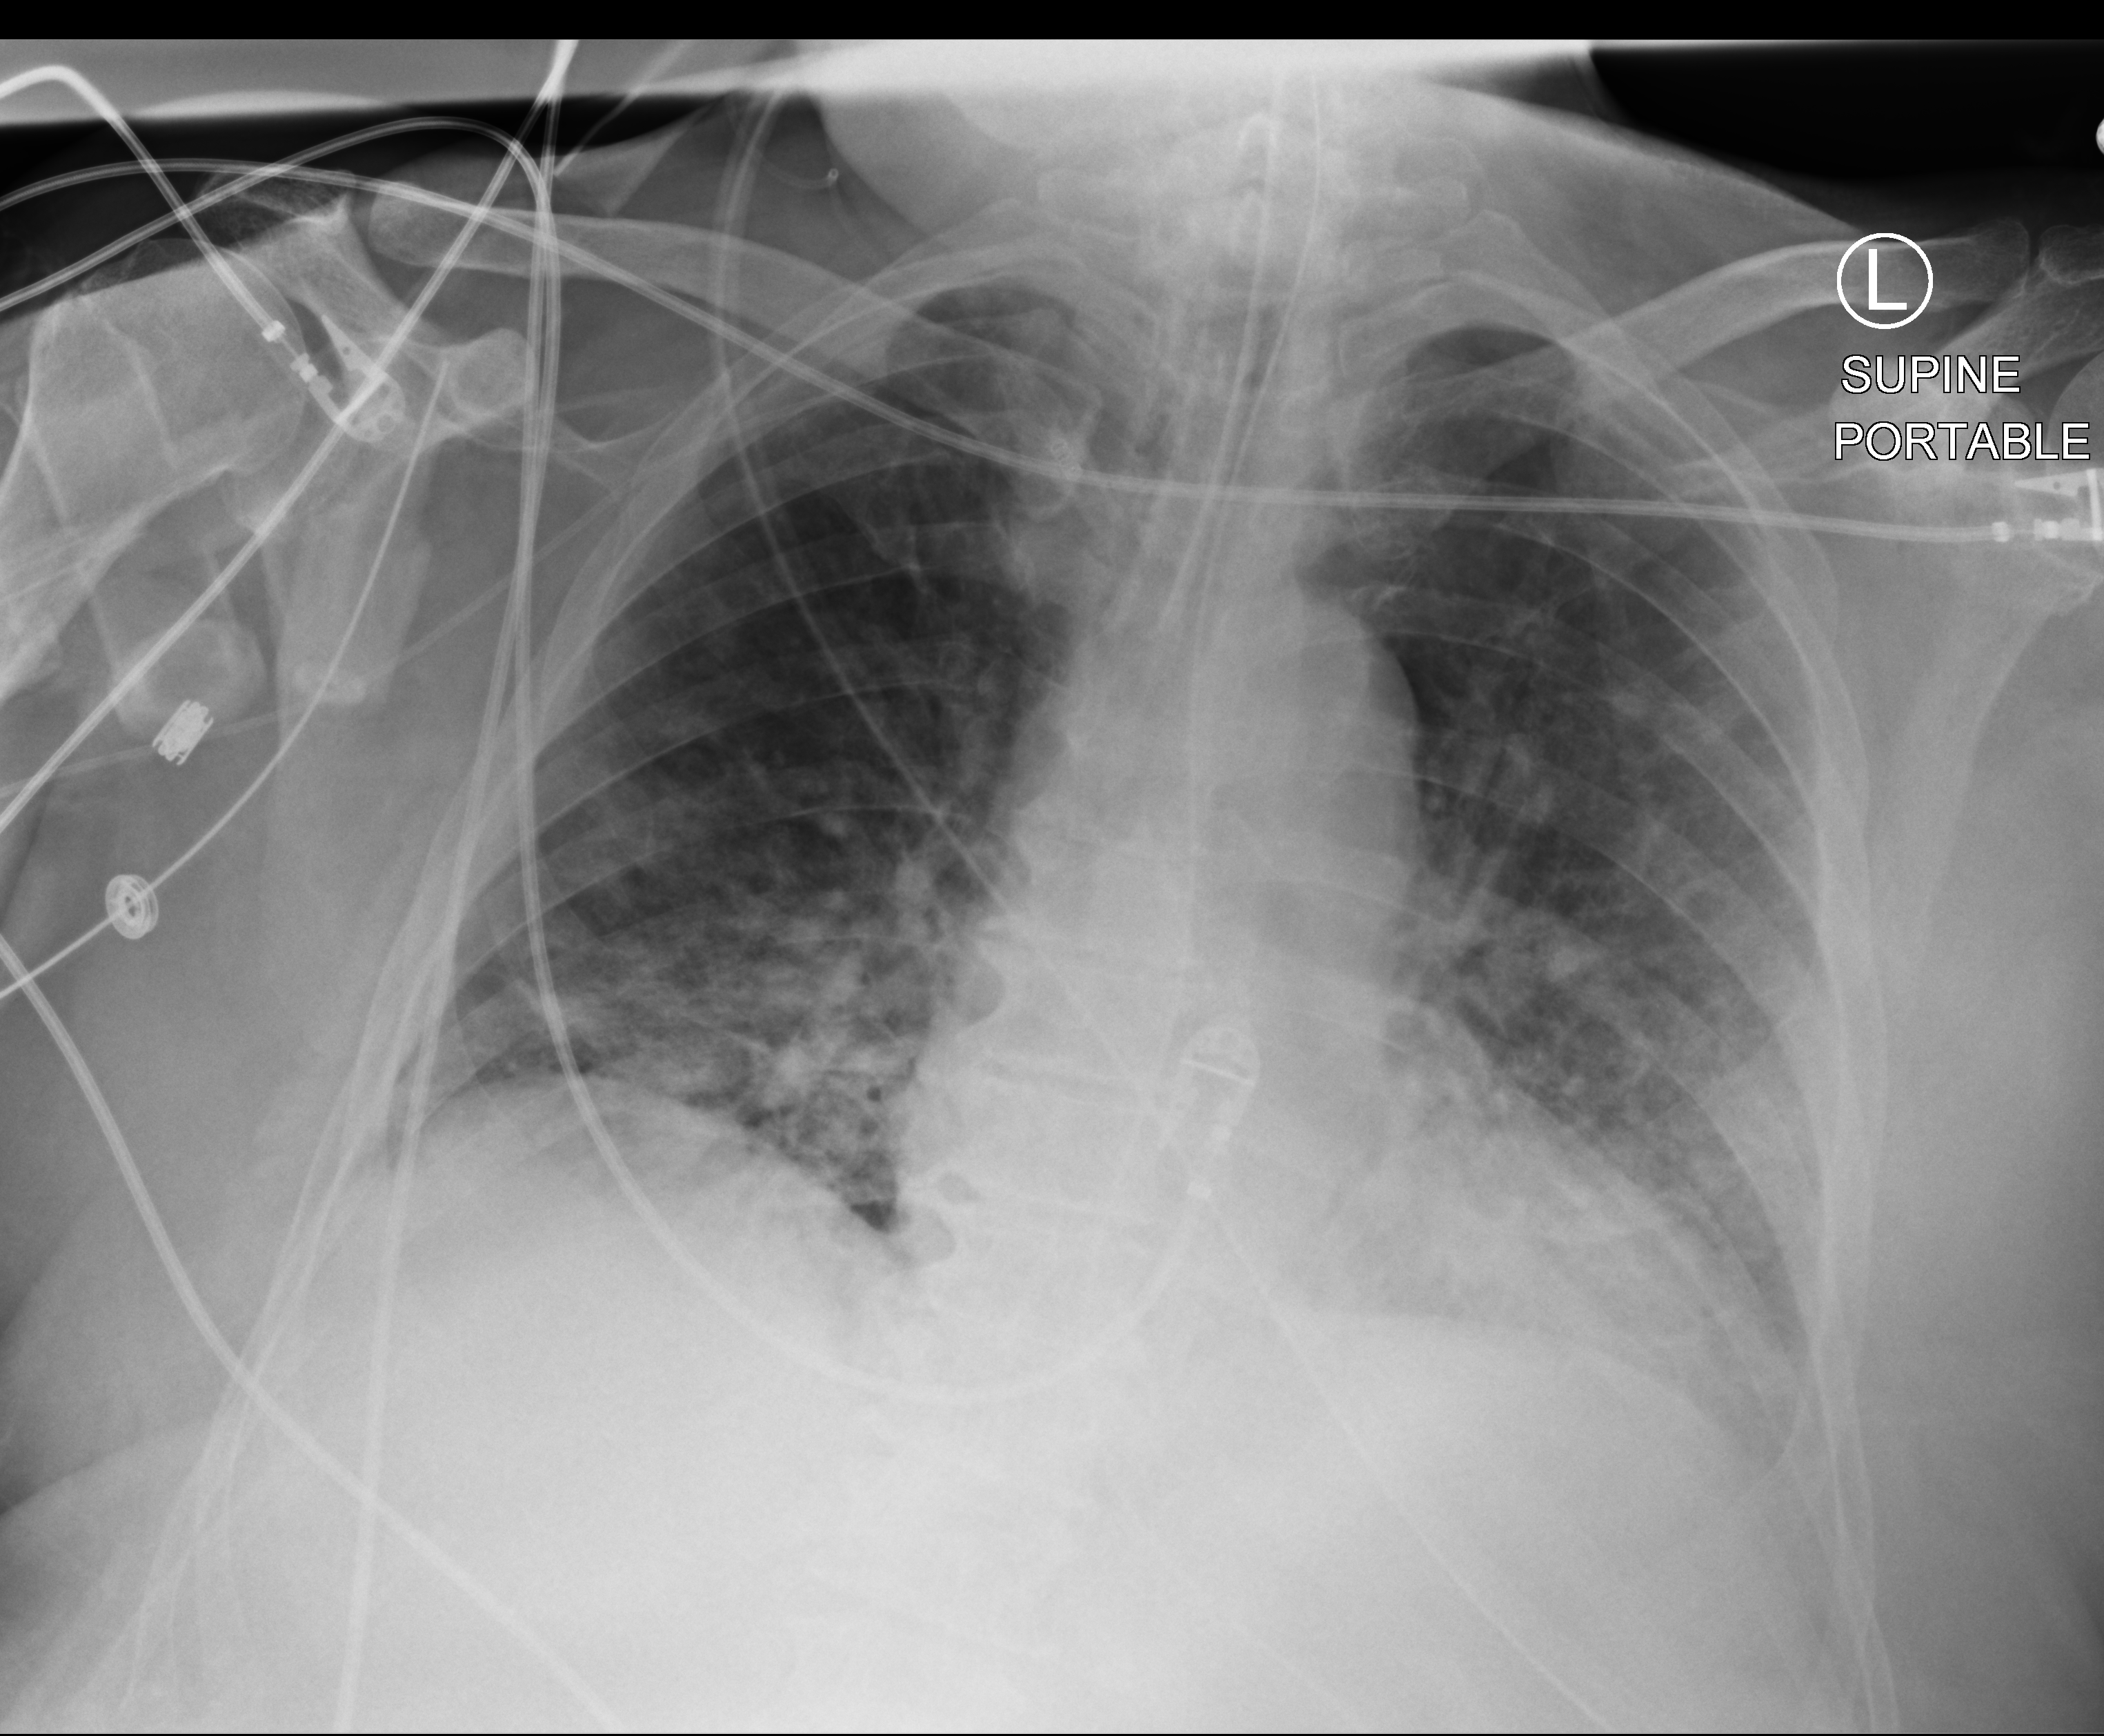
Bedside chest radiograph (computed radiography); anteroposterior (AP) projection. Patient hospitalised with COVID-19; male, aged 60–74 years.
Admission-level facts for this patient (not findings on this image; timing relative to this image not recorded): admitted to intensive care during this hospital stay: yes; mechanically ventilated during this hospital stay: yes.